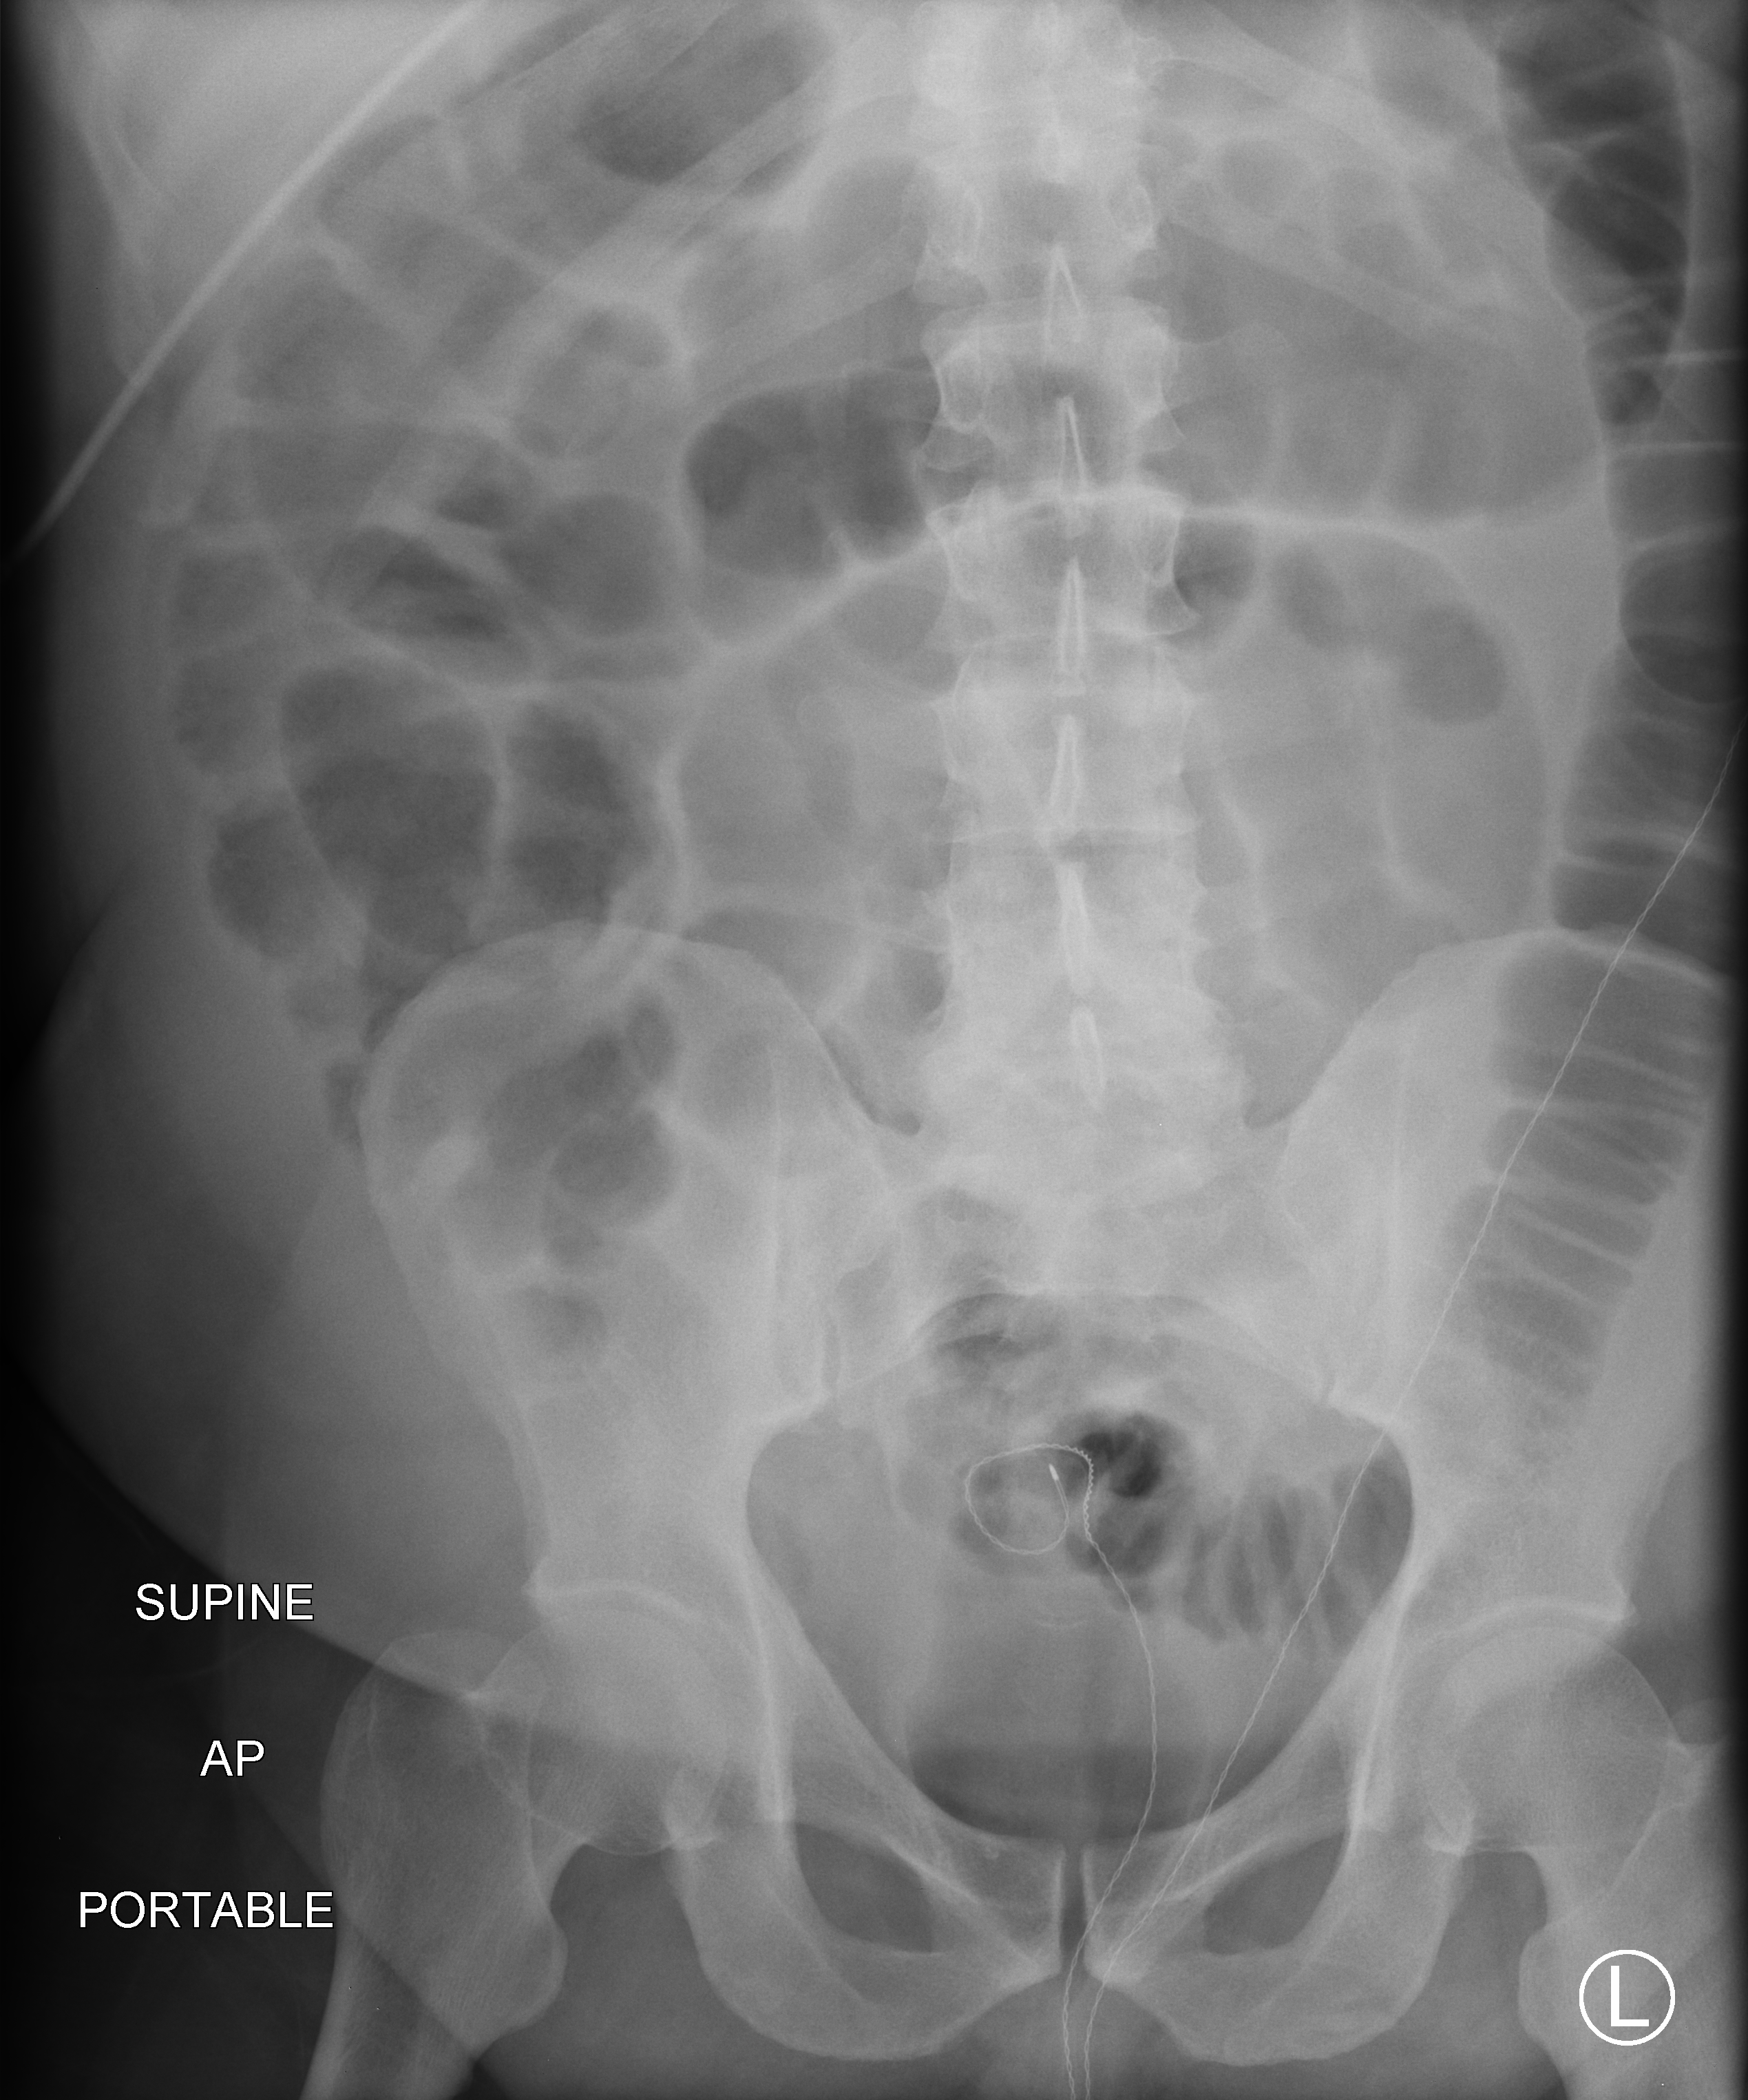
Abdomen X-ray (portable). Male patient hospitalised with COVID-19, age 18–59 years.
From the hospital-stay record, not from the radiograph (when in the stay this image was taken is not recorded): smoking status (admission record): never.